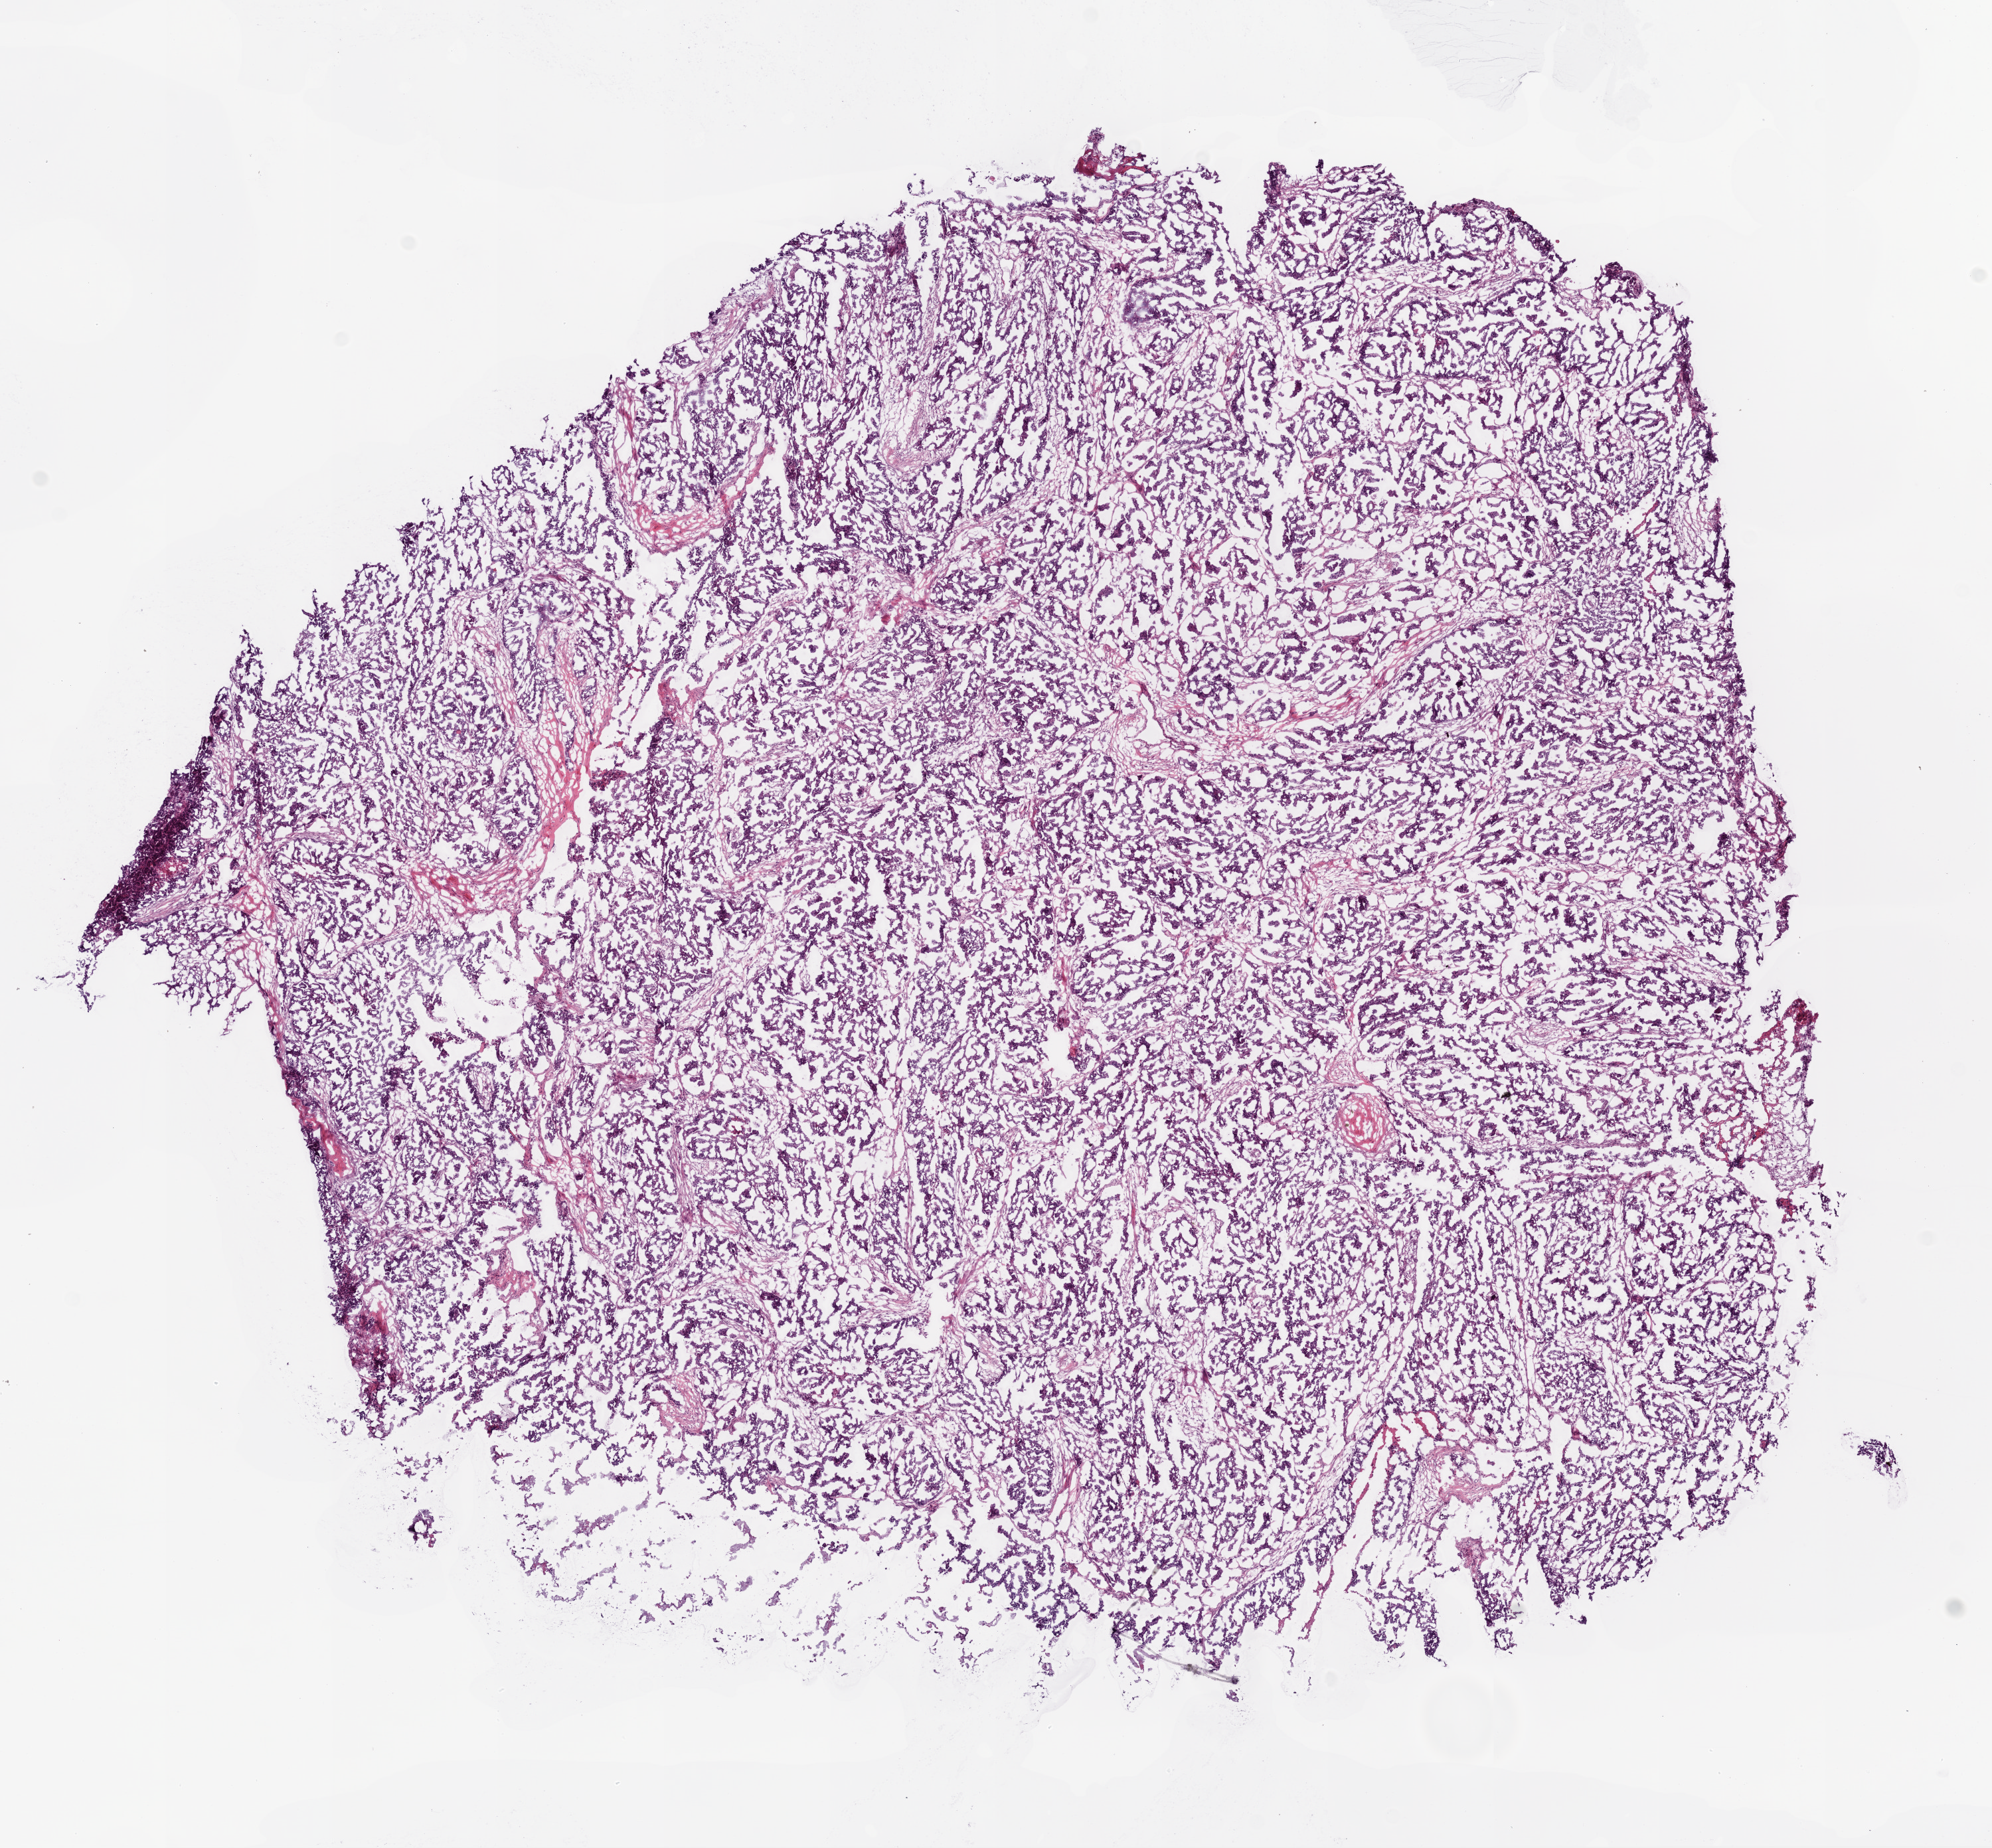
Digitized H&E-stained tissue section (whole slide) — whole scanned area (about 12.0 x 11.2 mm, slide scanned at 20x) shown as a low-resolution overview; frozen section; primary tumour sample from the ovary. Female, age 69 years at initial diagnosis. Histologic grade: G3 (poorly differentiated). Composition of this section per pathologist review: tumour cells 94%, tumour nuclei 97%, normal cells 5%, stromal cells 0%, necrosis 1%.
FIGO stage: IIIC. Histologic diagnosis: Serous cystadenocarcinoma, NOS.